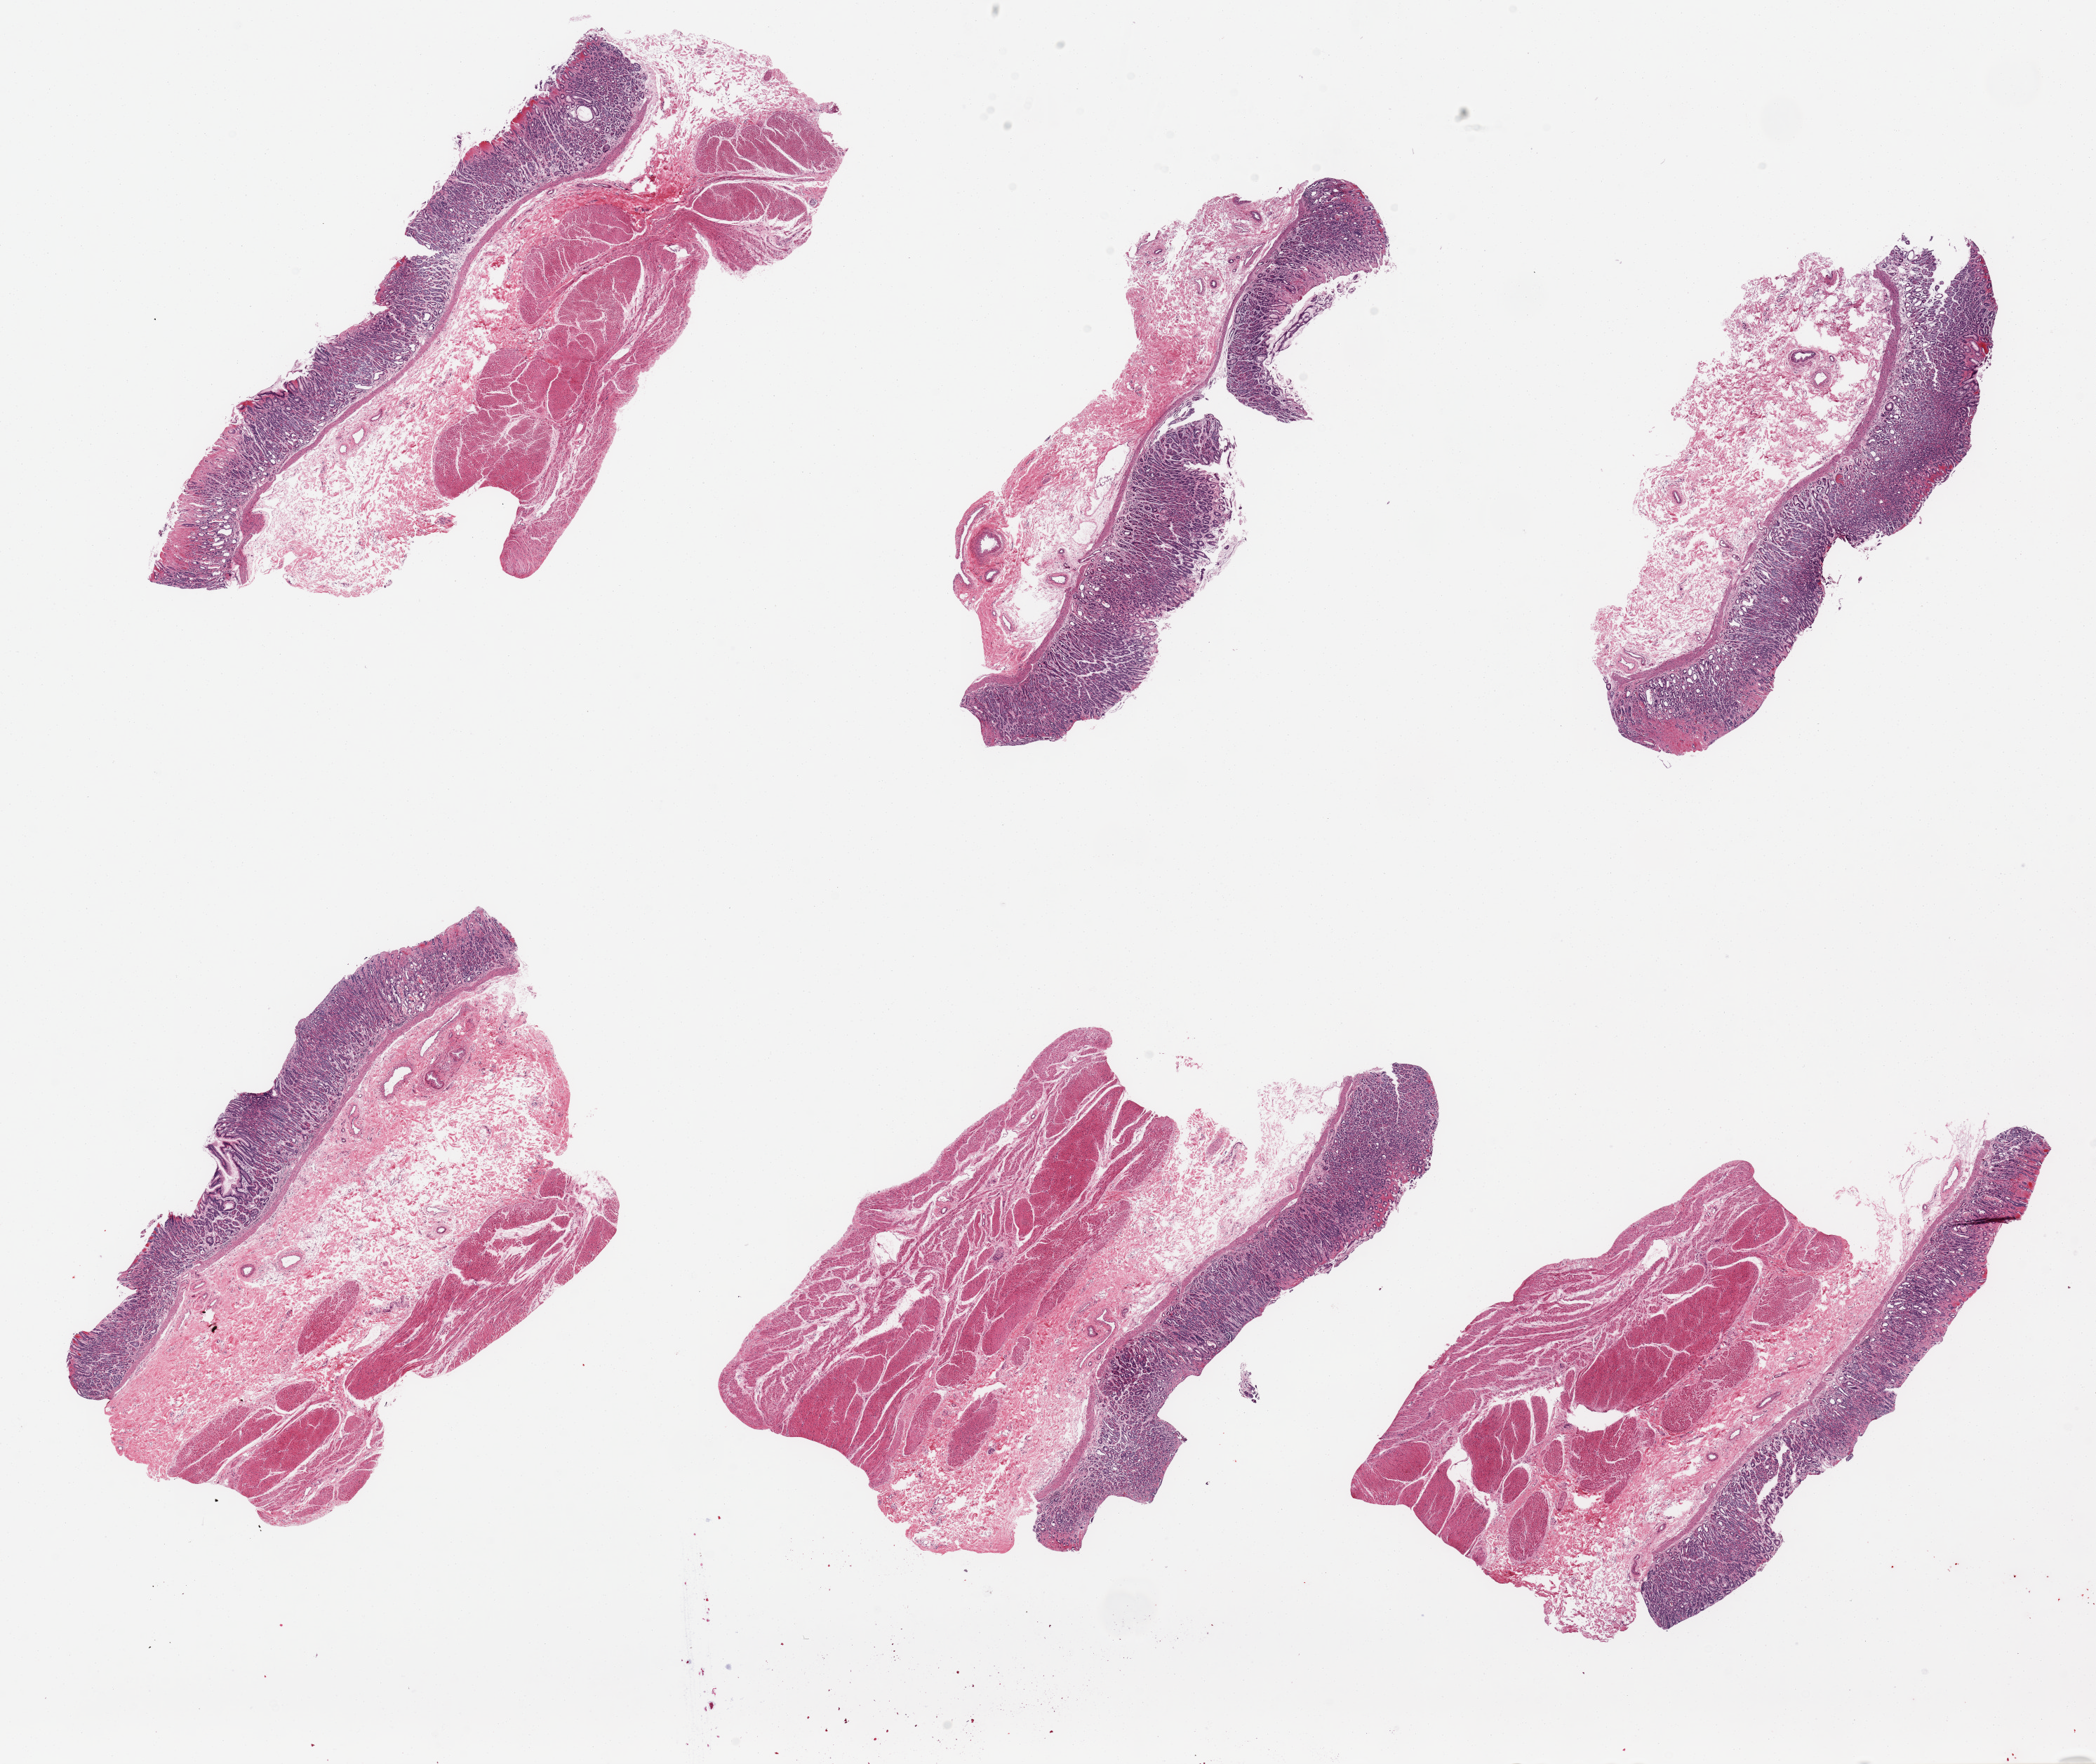
Whole-slide image, haematoxylin and eosin stain, shown as a low-resolution overview of the whole scanned area (about 23.6 x 19.9 mm). PAXgene-fixed, paraffin-embedded tissue. Sampled site (target tissue): stomach. Donor tissue sample.
- review note (as recorded): 6 pieces; variable representation of mucosa, submucosa, muscularis; multiple erosions, dilated deep glands